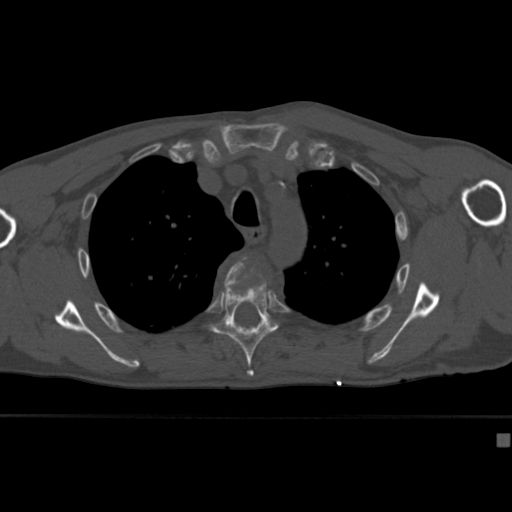
CT including the spine, one axial slice. Slice 311 of 430 in the series (ordered by position). Reconstruction kernel Br40s. Bone window (W 1800 / L 400 HU). 1.5 mm slice thickness. 512 × 512 image matrix, field of view 337 × 337 mm. Male patient, age 64 years. Case-level facts recorded for this patient, not image findings: primary cancer: uterus; vertebrae with lytic lesions (as recorded): T1, T4, T5, T7, L5.
Annotated regions visible in this slice (semi-automatically segmented with operator editing):
- T4 vertebra: bounding box [x1, y1, x2, y2] px = [225, 257, 262, 284]
- T5 vertebra: [209, 278, 279, 377]